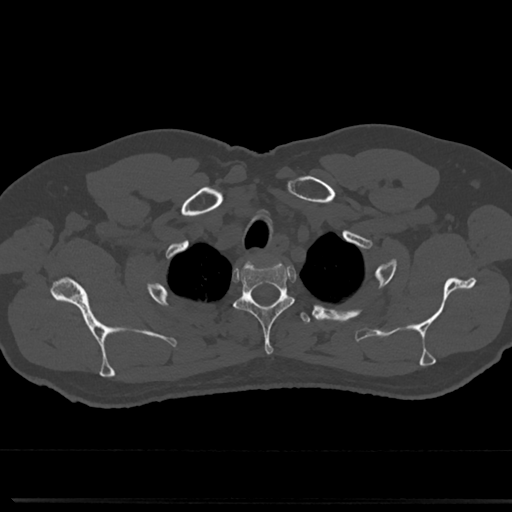
CT including the spine, one axial slice; 120 kVp; bone window (W 1800 / L 400 HU); 512 × 512 image matrix. Male patient, age 61 years. Case-level facts recorded for this patient, not image findings: primary cancer: prostate.
Annotated regions visible in this slice (semi-automatic segmentation, software-assisted and operator-edited):
- T2 vertebra: bounding box (x1, y1, x2, y2) in pixels: (235, 254, 294, 356)
- T3 vertebra: (296, 312, 311, 326)